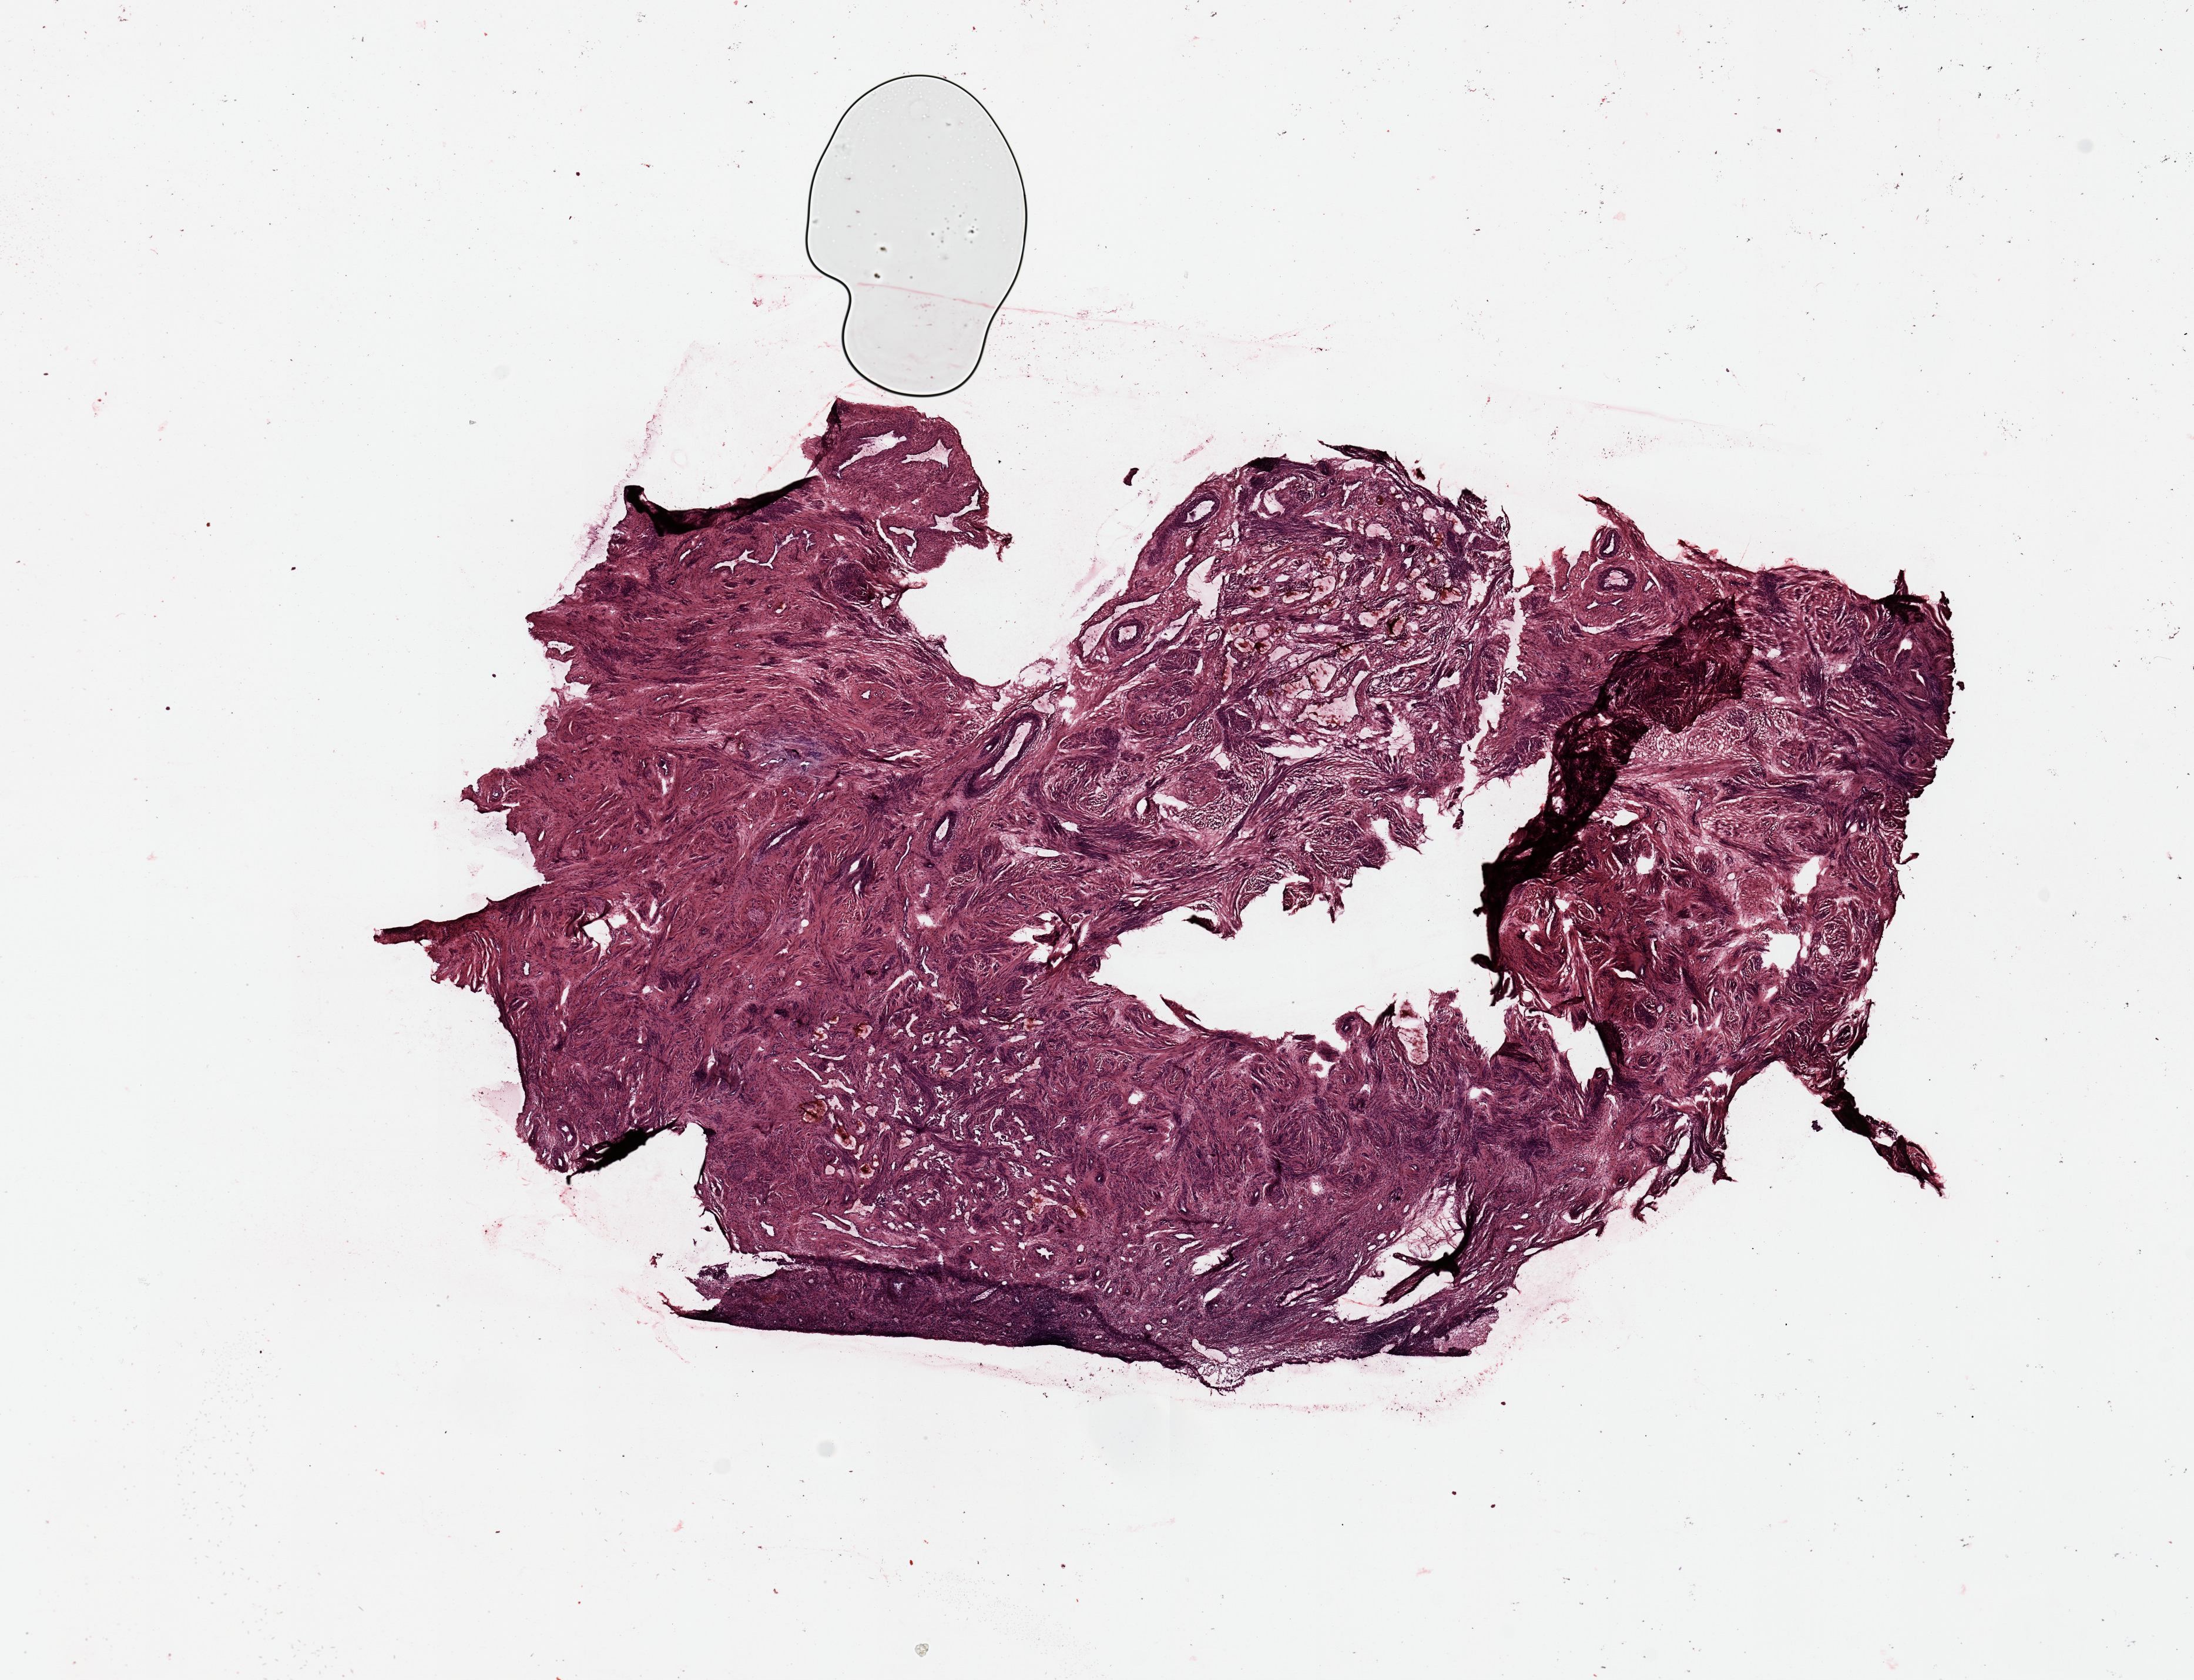
Whole-slide histology image, Hematoxylin and eosin (H&E) stained — shown as a low-resolution overview of the whole scanned area (about 14.8 x 11.3 mm). Uterus, normal (non-tumour) tissue. Patient: female, age 62 years.
* this section: normal (non-tumour) tissue from the same patient
* patient diagnosis: Endometrioid adenocarcinoma, NOS